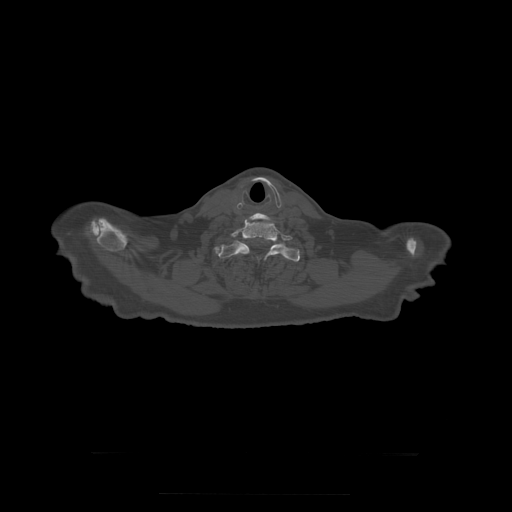
CT including the spine, one axial slice. Slice 294 of 397 in the series (ordered by position). Reconstruction kernel STANDARD. 120 kVp. Bone window (W 1800 / L 400 HU). 1.25 mm slice thickness. 512 × 512 image matrix, field of view 510 × 510 mm. Patient age 73 years. From the clinical record (not read from this slice): primary cancer: prostate.
Outlined on this slice (semi-automatic segmentation, software-assisted and operator-edited):
- T1 vertebra: bounding box (x1, y1, x2, y2) in pixels: (217, 241, 300, 265)